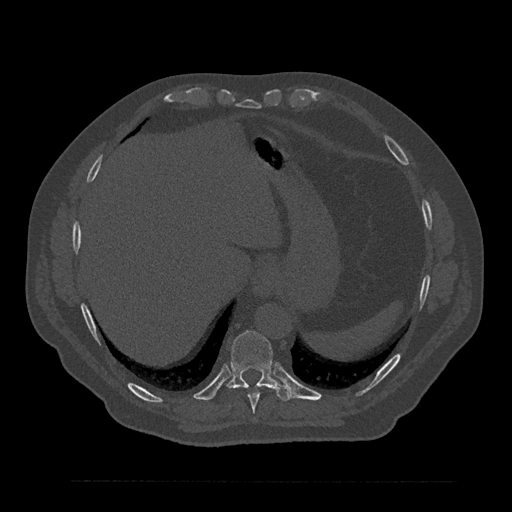
CT including the spine, one axial slice. Position 372 of 797 along the scan axis. 120 kVp. Bone window (W 1800 / L 400 HU). 0.5 mm slice thickness. 512 × 512 image matrix, field of view 430 × 430 mm. Male patient, age 61 years. From the clinical record (not read from this slice): primary cancer: prostate.
Annotated regions visible in this slice (semi-automatic segmentation, software-assisted and operator-edited):
- T10 vertebra: bounding box [x1, y1, x2, y2] px = [227, 331, 293, 401]
- T9 vertebra: [247, 384, 267, 413]